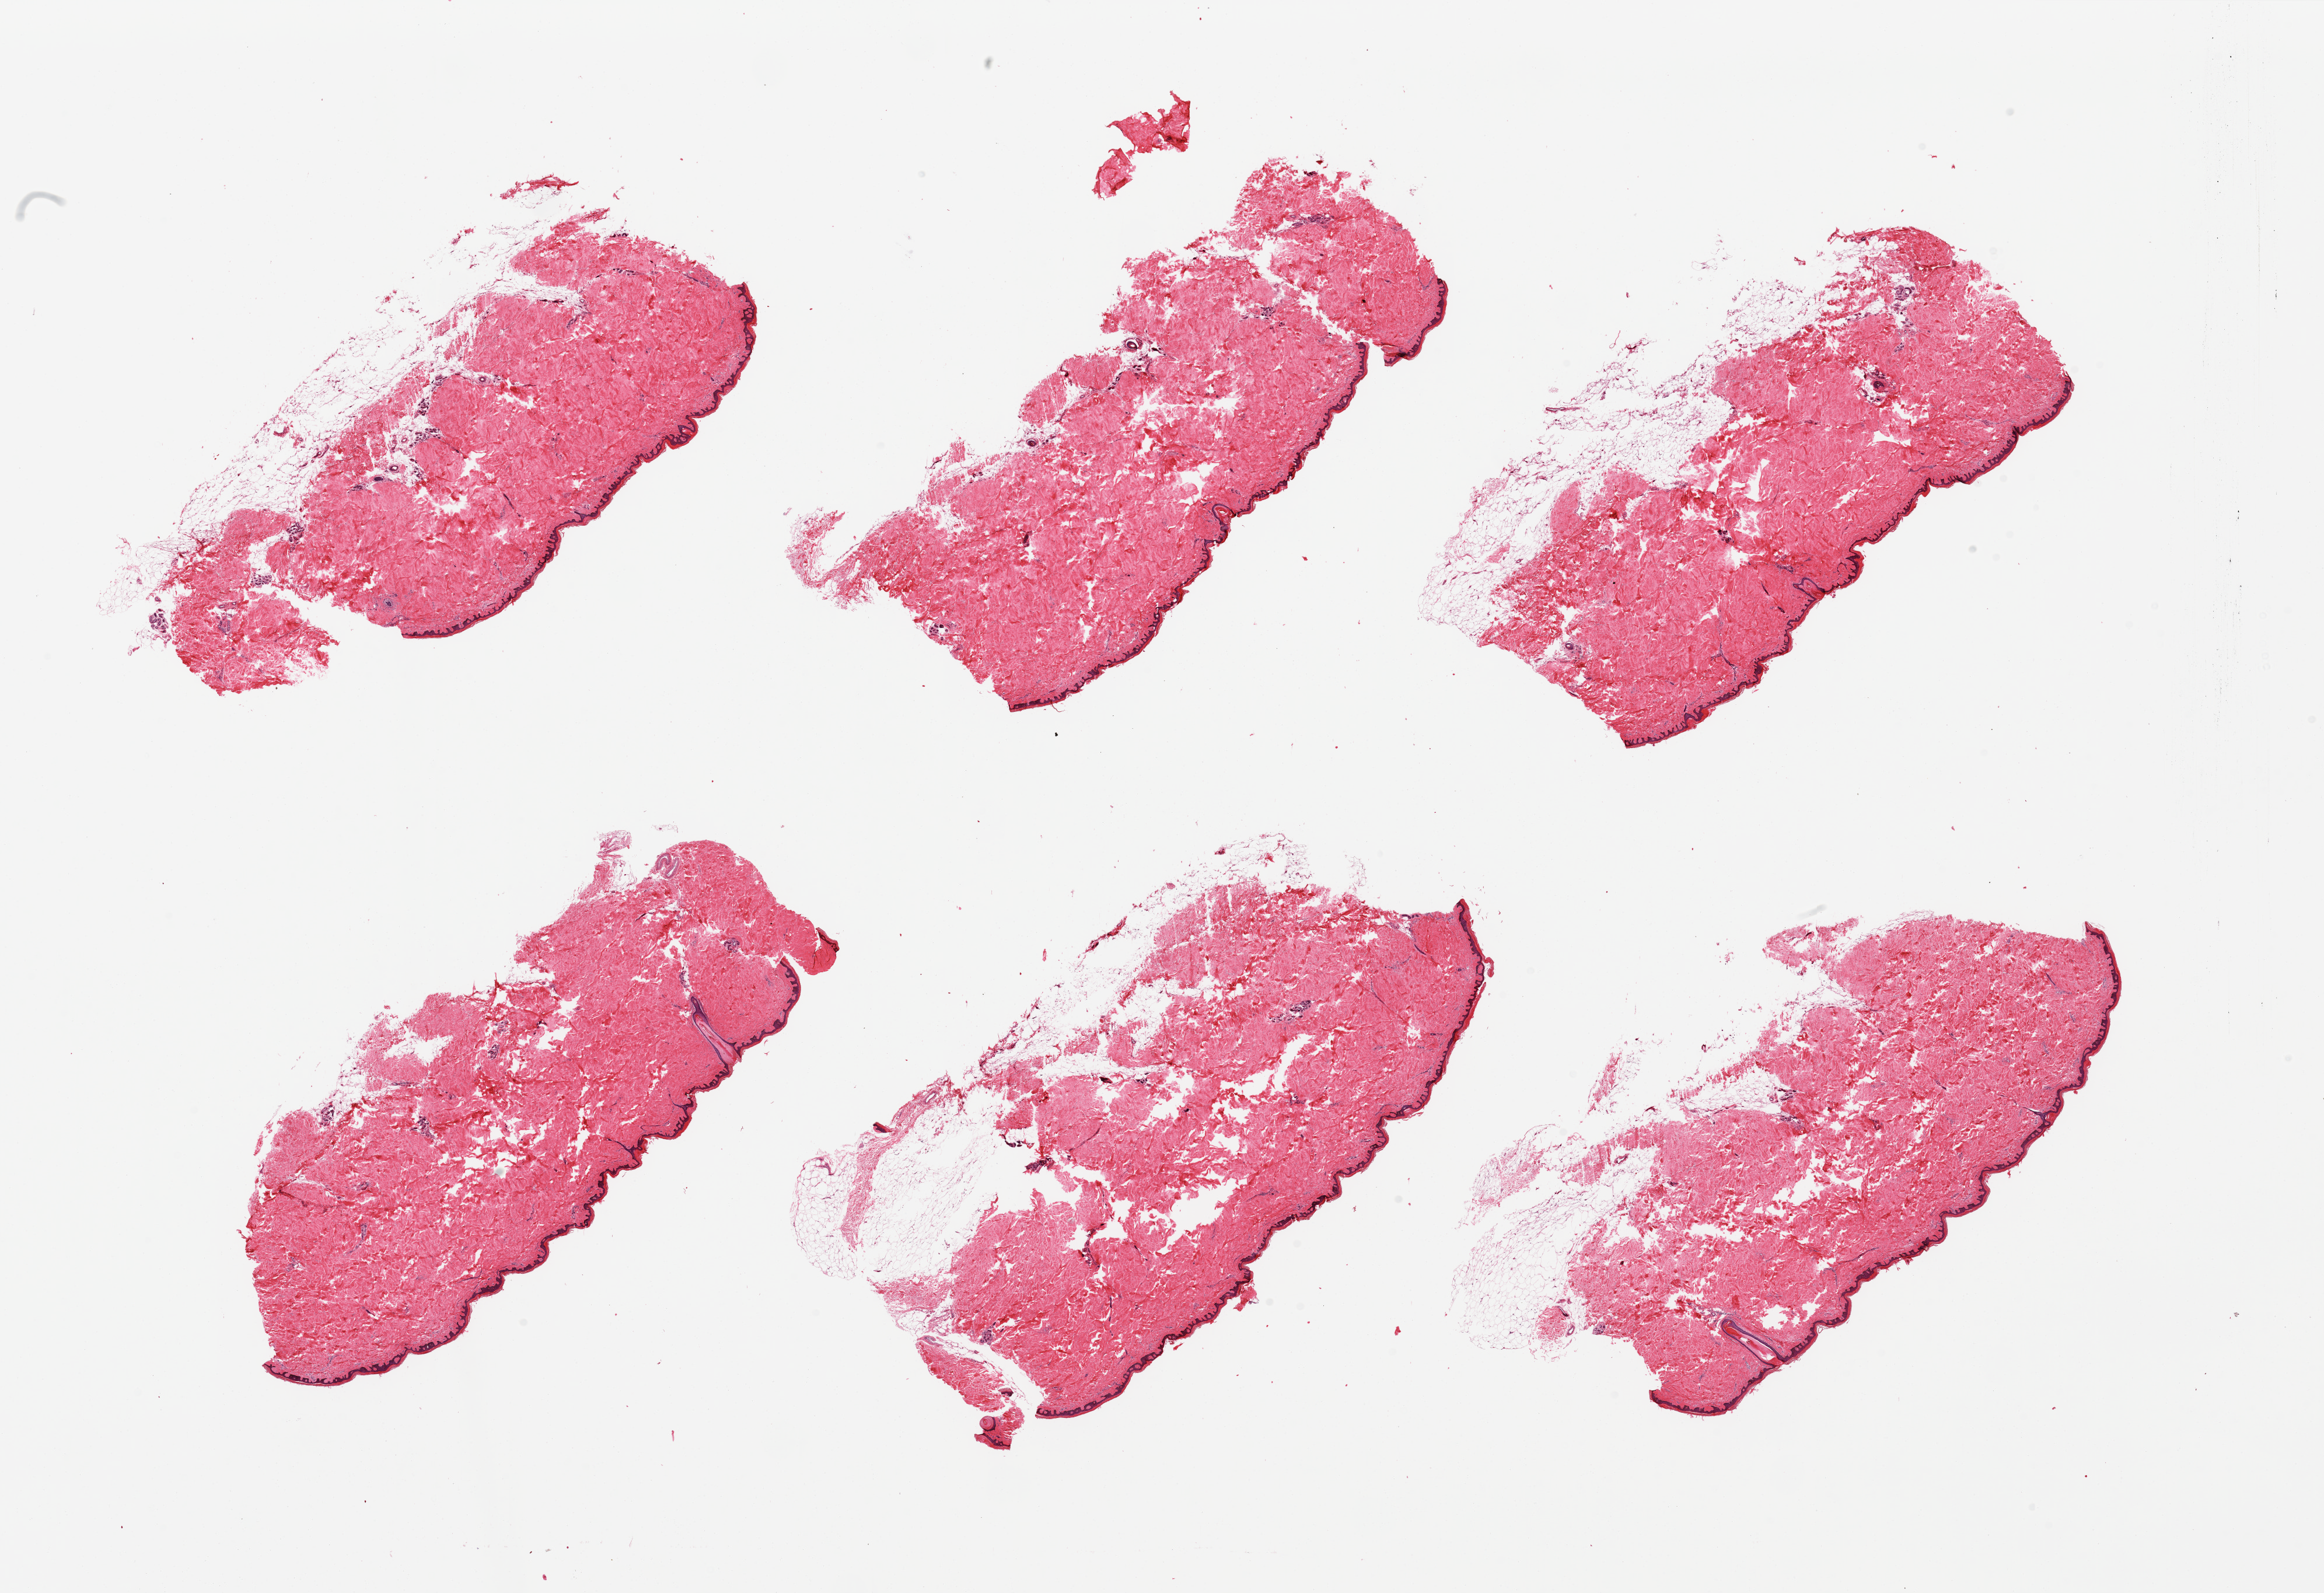
Whole-slide image, haematoxylin and eosin stain — a low-resolution overview of the entire scanned area, about 31.5 x 21.6 mm, PAXgene-fixed, paraffin-embedded tissue, target tissue: skin of lower leg, donor tissue sample. Donor sex: female.
• reviewer comment on this tissue sample: 6 pieces; subcutaneous fat on 4 of 6 pieces up to 1.5mm thick. 10% intradermal fat